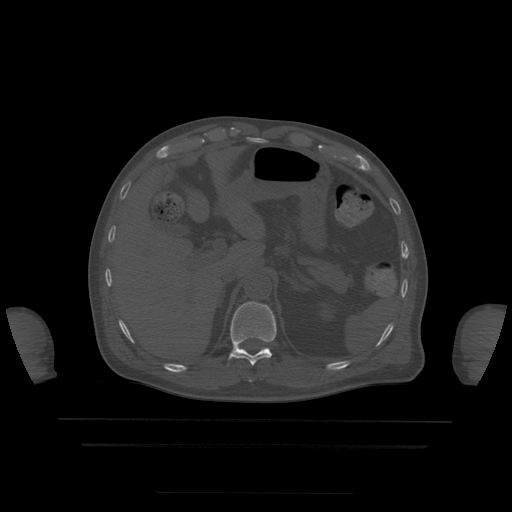
CT including the spine, one axial slice. Slice 217 of 522 in the series (ordered by position). Bone window (W 1800 / L 400 HU). 512 × 512 image matrix, field of view 436 × 436 mm. Patient age 68 years. From the clinical record (not read from this slice): primary cancer: urothelial.
Outlined on this slice (semi-automatic segmentation, software-assisted and operator-edited):
- T11 vertebra: box from (x=229, y=302) to (x=277, y=366) px